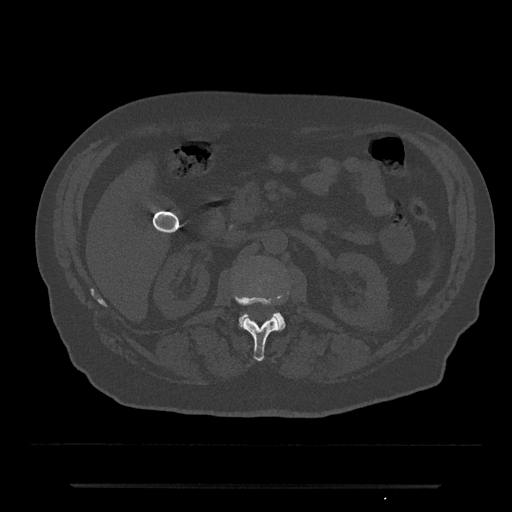
CT including the spine, one axial slice. Position 513 of 797 along the scan axis. Reconstruction kernel Br40s/3. 120 kVp. Bone window (W 1800 / L 400 HU). 0.5 mm slice thickness. 512 × 512 image matrix. Patient: male, 80 years. From the clinical record (not read from this slice): primary cancer: prostate.
Structures marked on this image (semi-automatically segmented with operator editing):
- L1 vertebra: bounding box <235,296,280,361> (left, top, right, bottom; pixels)
- L2 vertebra: <238,312,285,331>